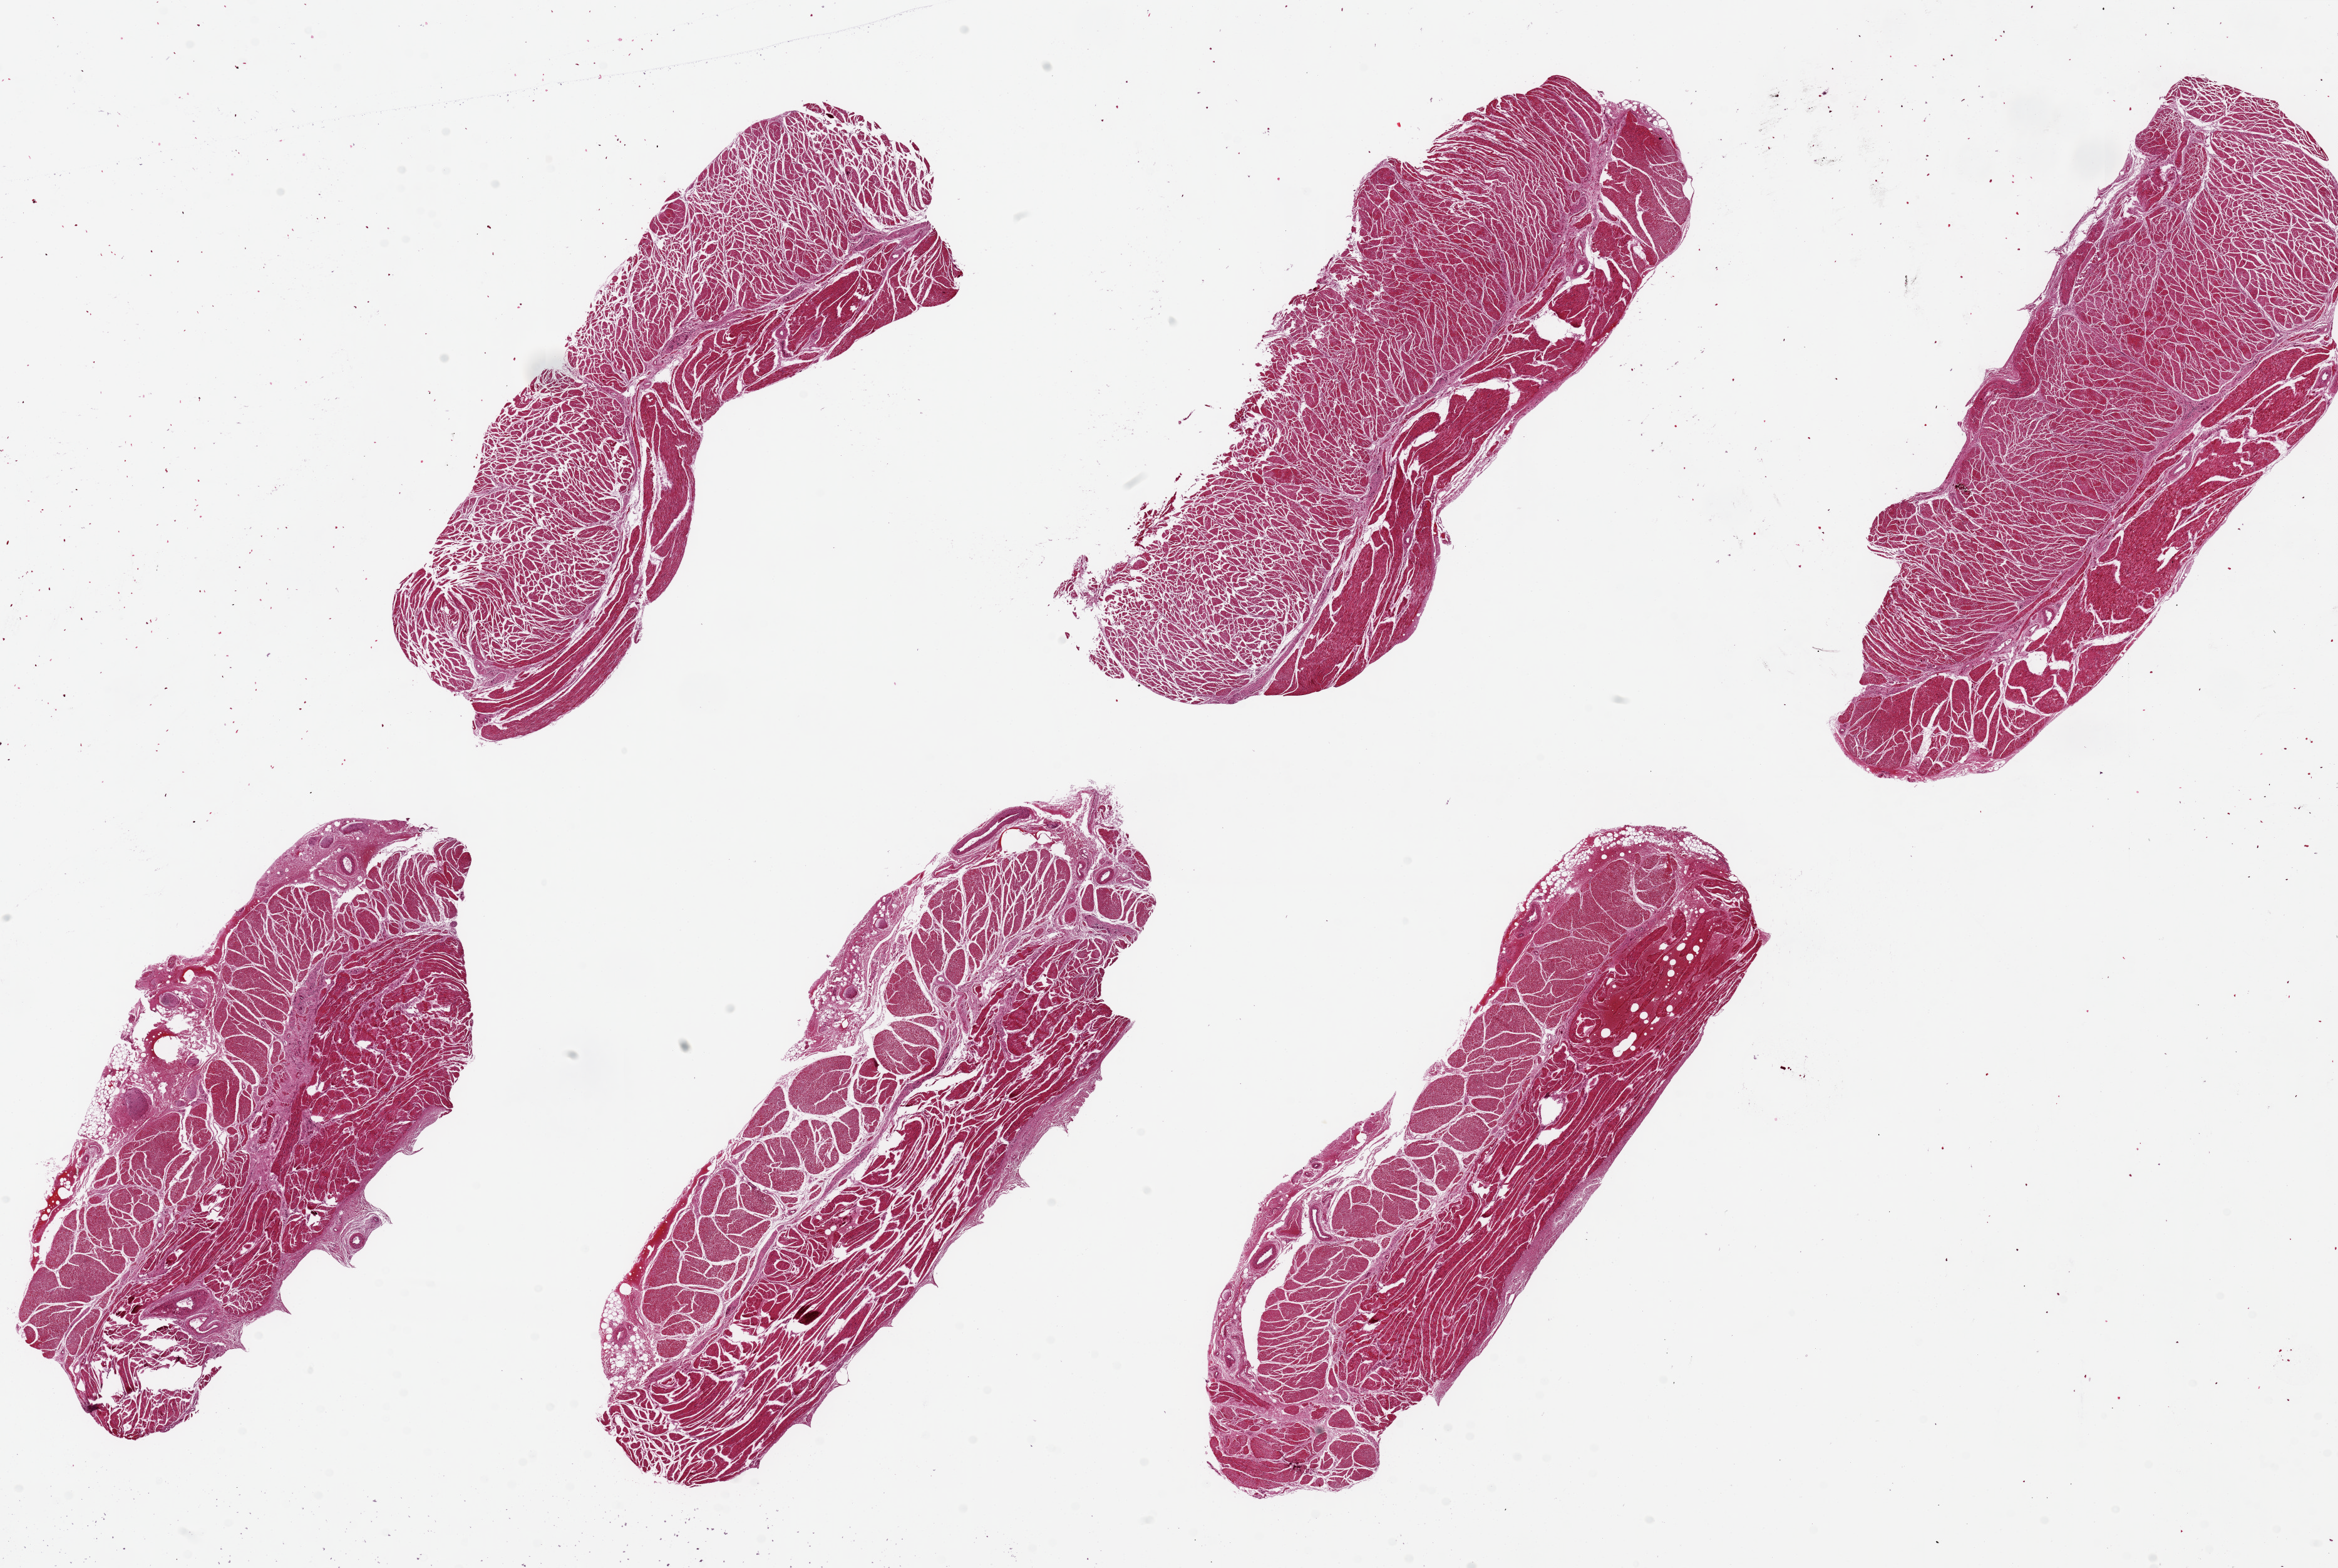
Digitized hematoxylin and eosin (H&E)-stained section — a low-resolution overview of the entire scanned area, about 29.5 x 19.8 mm; PAXgene-fixed, paraffin-embedded tissue; target tissue: esophageal muscle; tissue donor sample.
Review note (as recorded): 6 pieces ~10x3mm, all muscularis, good specimens.